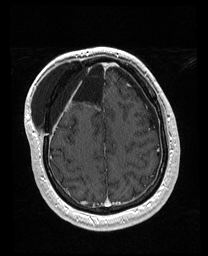
Brain MRI from a brain-tumour surgery series, one axial slice. Slice 53 of 176 in the series (ordered by position). T1-weighted post-contrast. 1 mm slice thickness. 208 × 256 image matrix, field of view 208 × 256 mm. From the clinical record (not read from this slice): histopathology: Astrocytoma; WHO grade: 4; IDH mutation: yes.
Outlined on this slice (expert manual segmentation):
- previous resection cavity: bounding box [x1, y1, x2, y2] px = [62, 60, 93, 103]